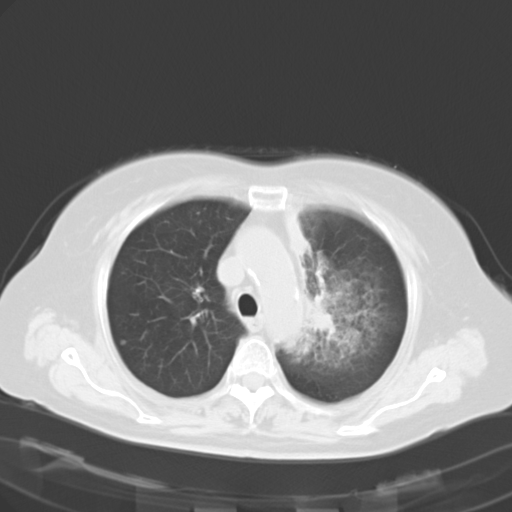
Chest CT, one axial slice. Slice 20 of 27 in the series (ordered by position). 120 kVp. Lung window (W 1500 / L -600 HU). 10 mm slice thickness. 512 × 512 image matrix, field of view 353 × 353 mm. Female patient, age 65 years. From the clinical record (not read from this slice): clinical TNM (as recorded): T2b N1 M0.
Annotated regions visible in this slice (bounding box drawn by a radiologist):
- lung tumour (recorded histology: adenocarcinoma): box from (x=301, y=291) to (x=339, y=339) px